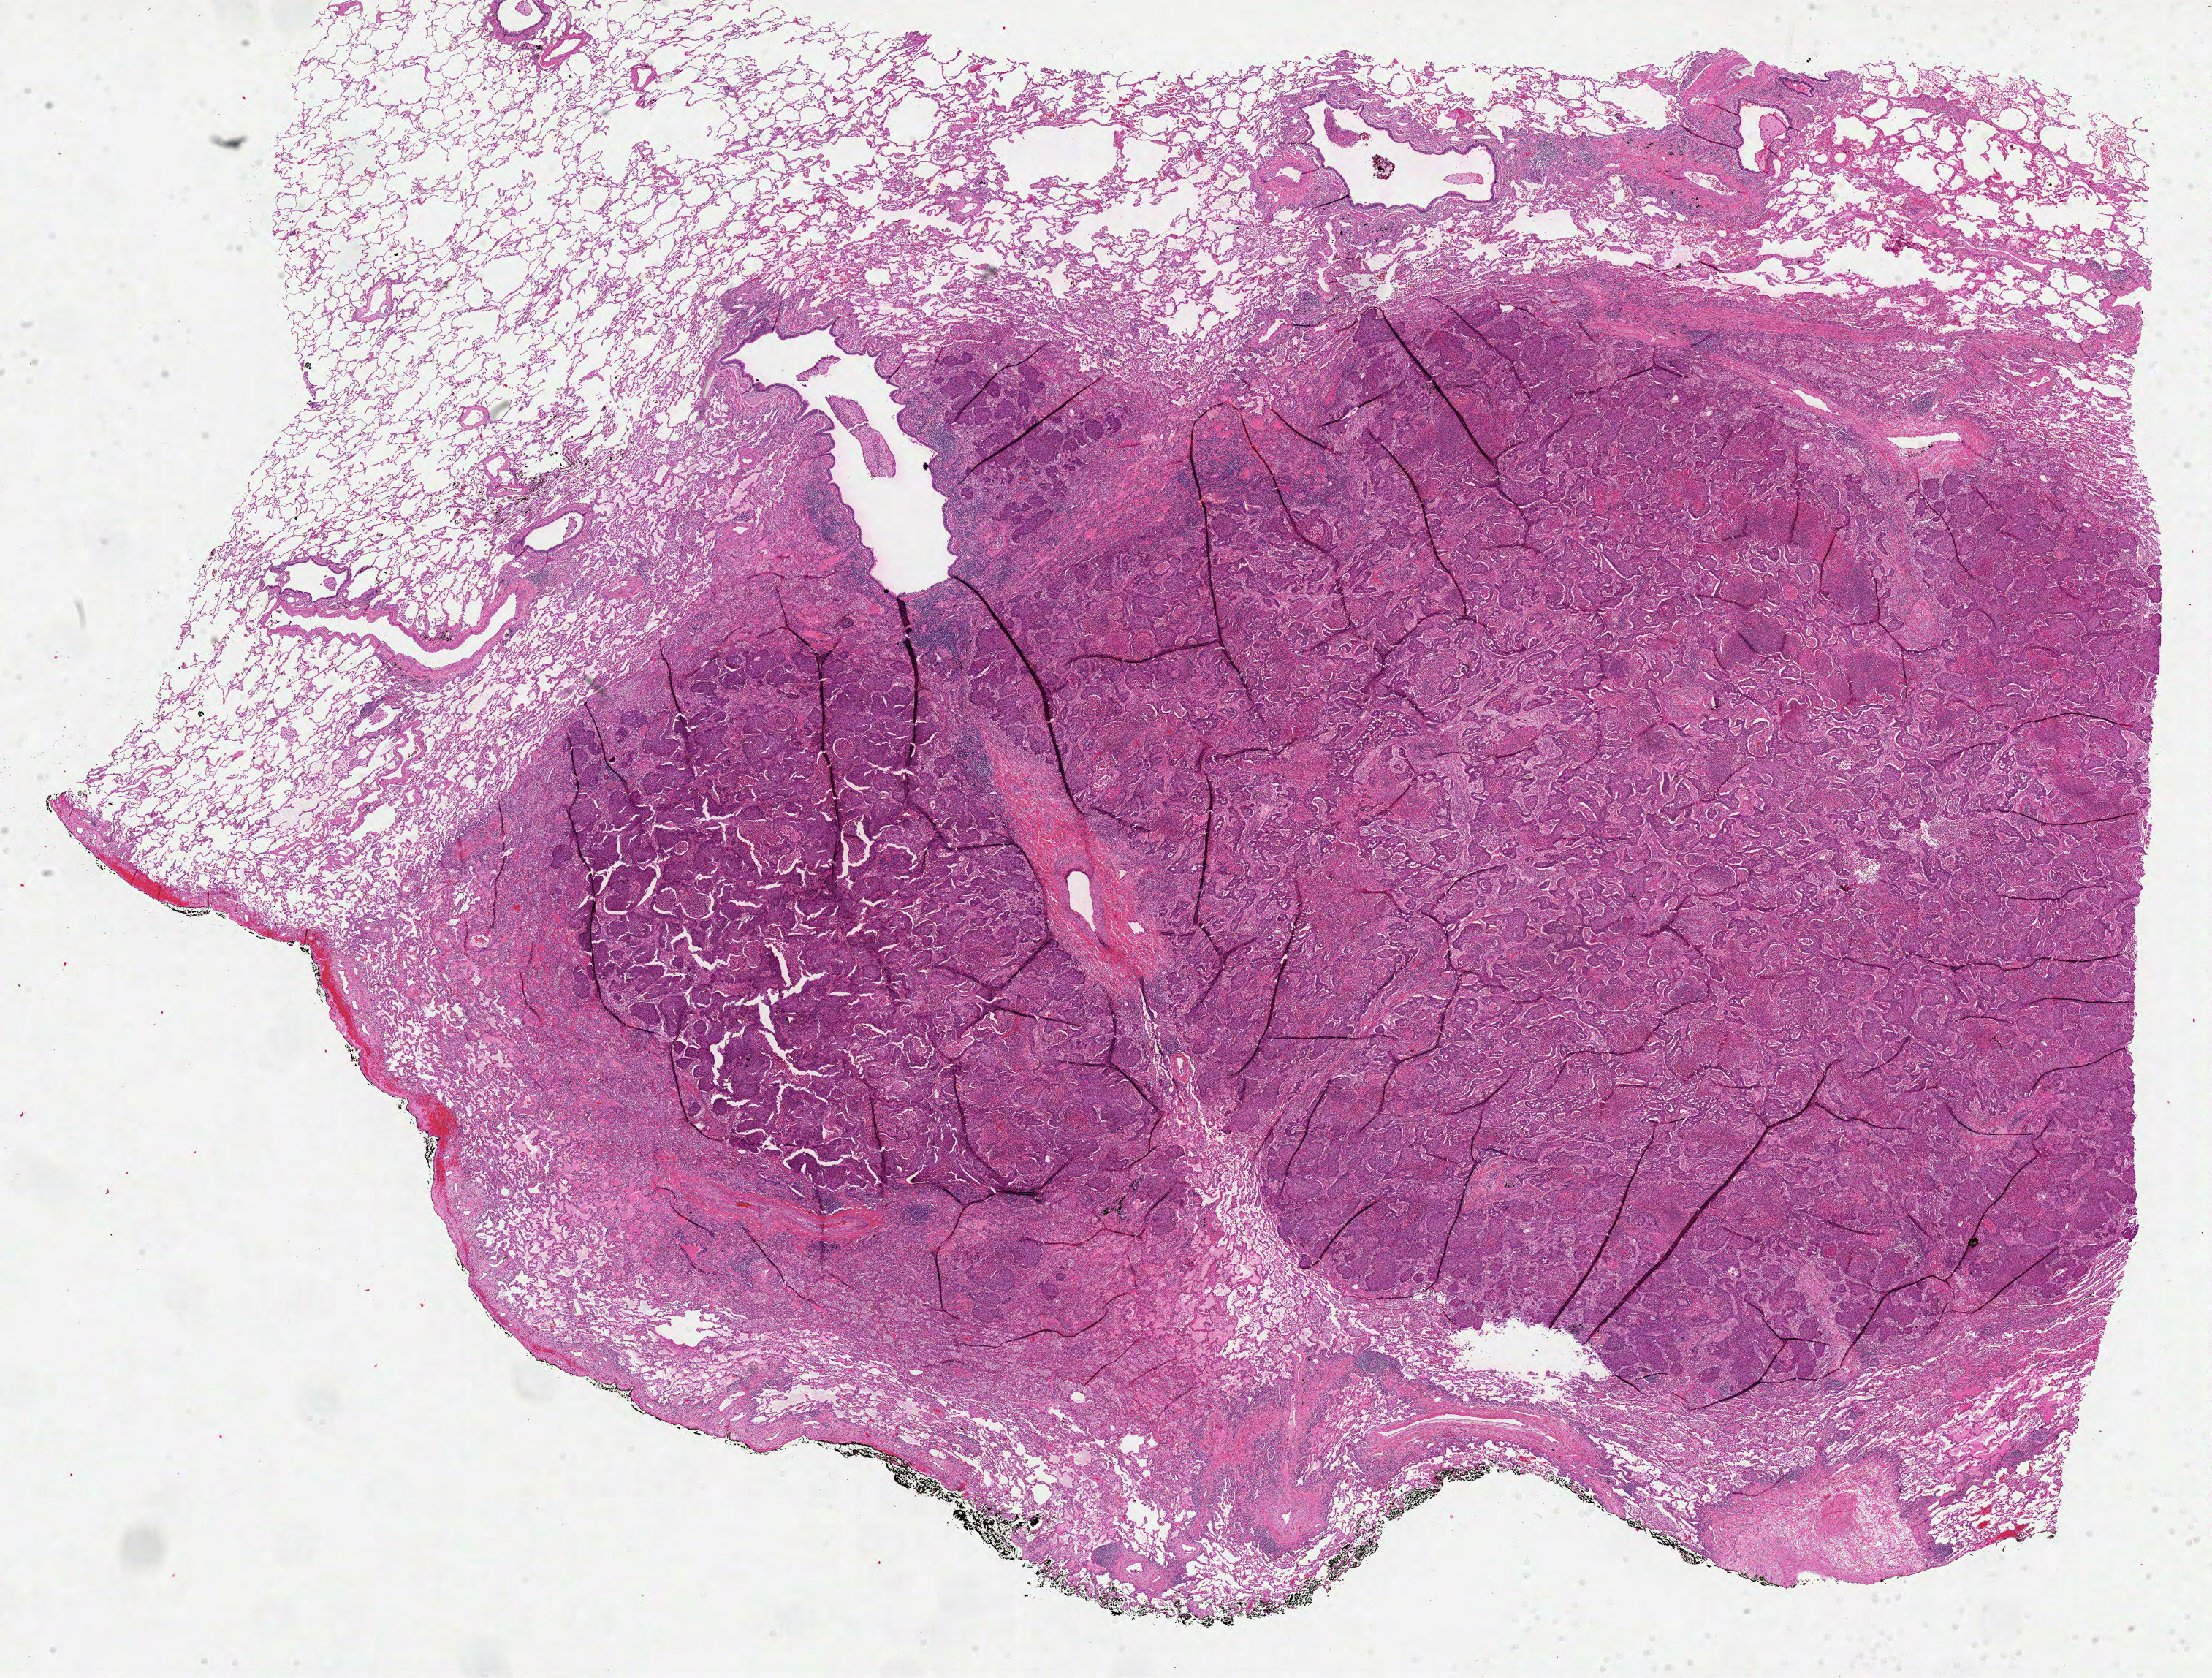
Digitized Hematoxylin and eosin (H&E) stained tissue section (whole slide), shown as a low-resolution overview of the whole scanned area (about 24.4 x 18.5 mm, slide scanned at 40x). Formalin-fixed paraffin-embedded (FFPE) diagnostic section. Lung, primary tumour sample. Male patient; age at initial diagnosis 57 years.
* diagnosis: Squamous cell carcinoma, NOS
* AJCC pathologic stage: IIIA (6th edition)
* TNM: T2 N2 M0